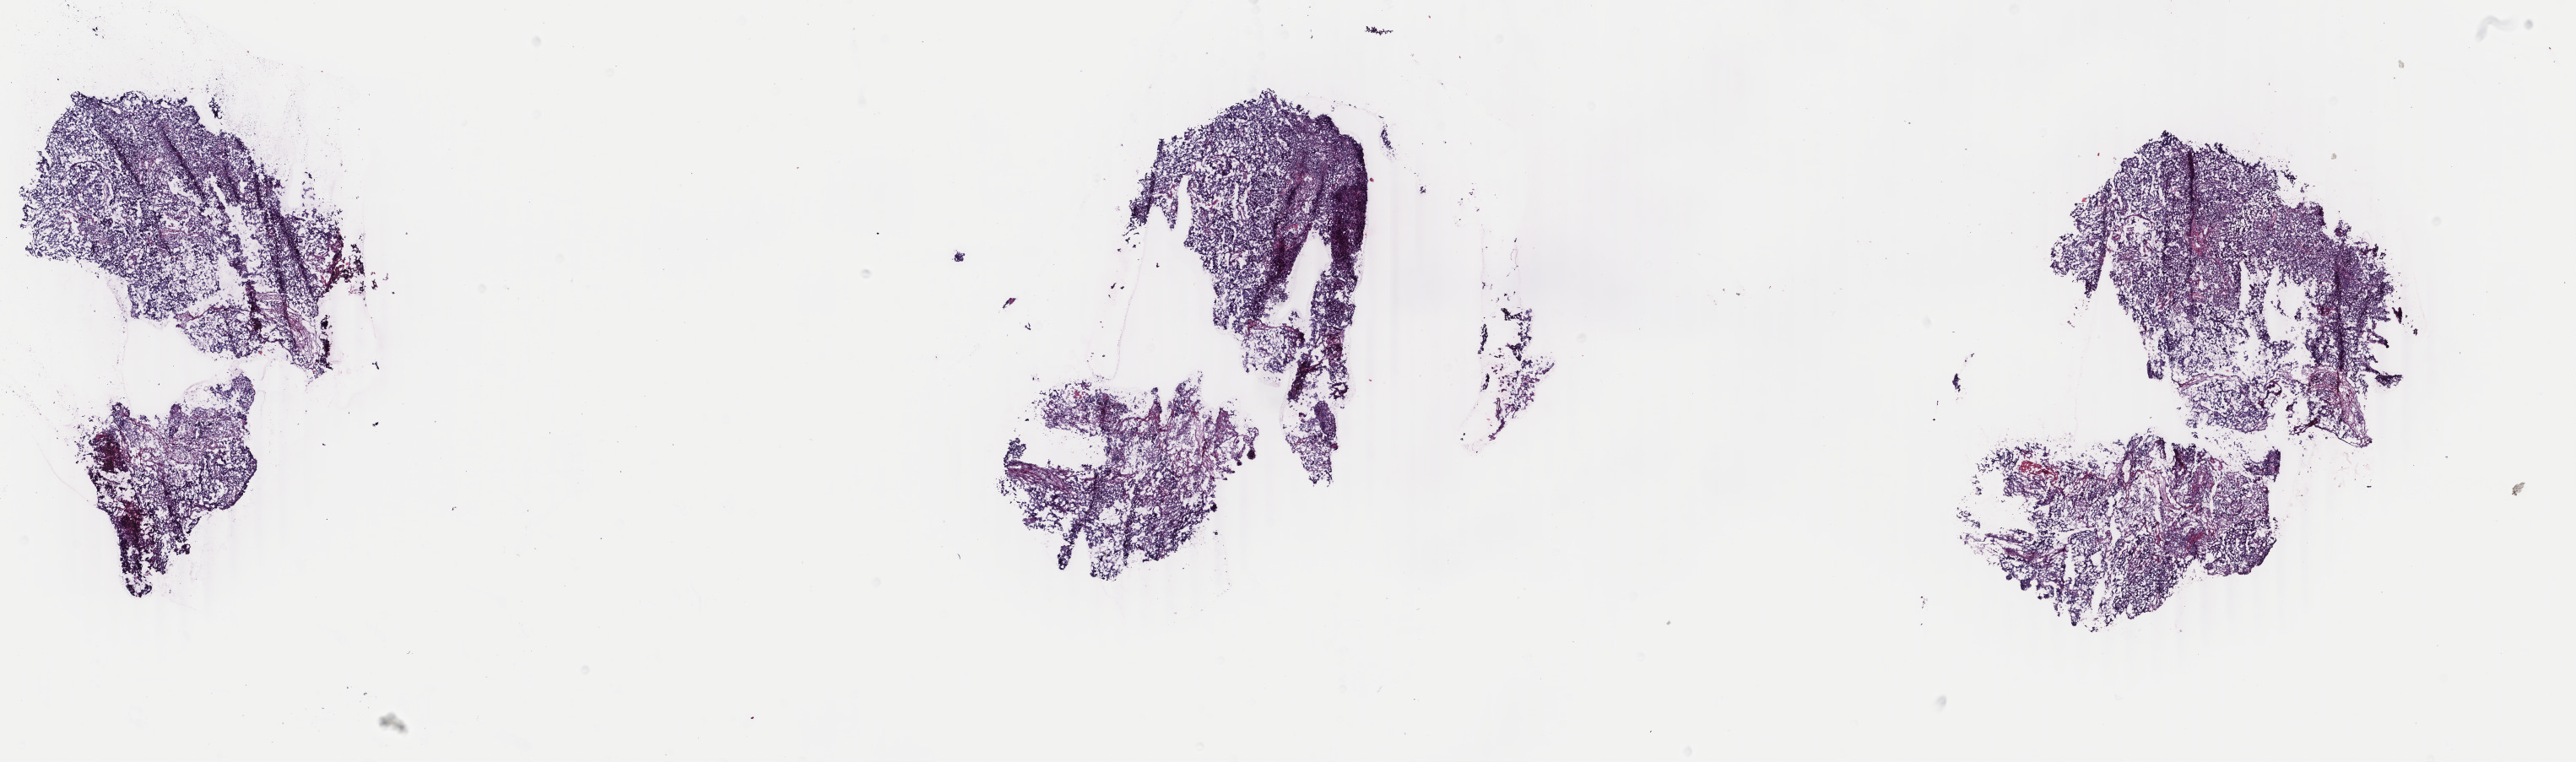
Whole-slide histology image, H&E — low-resolution overview of the scanned area, about 24.3 x 7.2 mm (slide scanned at 40x). Frozen section from the bottom of the tissue portion. Sample: primary tumour, uterus. Patient: female, age at initial diagnosis 46 years. Histologic grade: G3 (poorly differentiated). Pathologist review of this section (percent, as recorded): tumour cells 100%, tumour nuclei 90%, normal cells 0%, stromal cells 0%, necrosis 0%. Infiltration values recorded for this section: lymphocyte infiltration 0%, monocyte infiltration 0%, neutrophil infiltration 0%.
• FIGO stage: IA
• pathologic diagnosis: Endometrioid adenocarcinoma, NOS (endometrium)